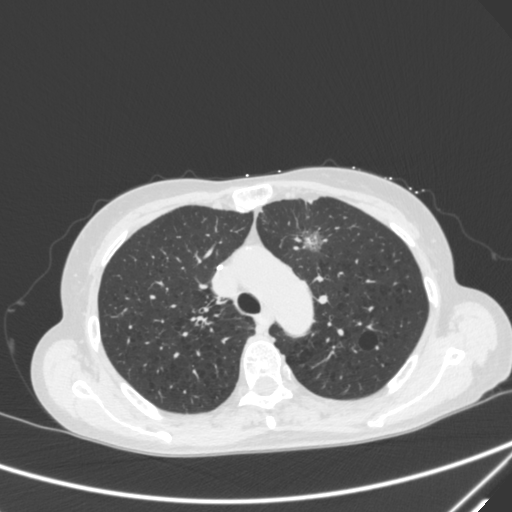
Chest CT, one axial slice. Slice 220 of 300 in the series (ordered by position). Lung window (W 1500 / L -600 HU). 1 mm slice thickness. 512 × 512 image matrix, field of view 350 × 350 mm. Female patient, age 71 years. From the clinical record (not read from this slice): clinical TNM (as recorded): T1c N0 M0; histopathological grade: G2-3.
Structures marked on this image (bounding box drawn by a radiologist):
- lung tumour (recorded histology: adenocarcinoma): box from (x=299, y=224) to (x=333, y=256) px